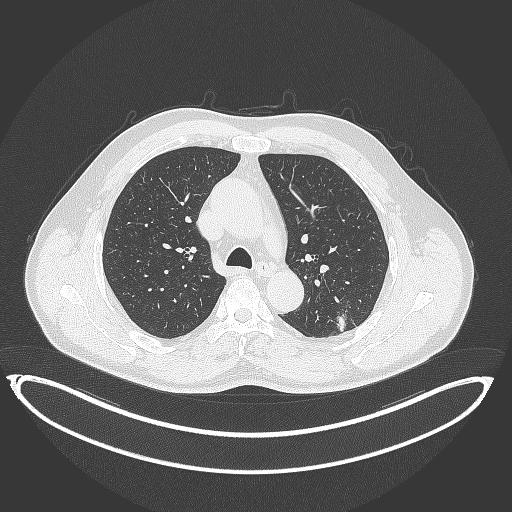
Chest CT, one axial slice; position 243 of 399 along the scan axis; lung window (W 1500 / L -600 HU); 1 mm slice thickness; 512 × 512 image matrix, field of view 469 × 469 mm. Male patient, age 58 years. From the clinical record (not read from this slice): clinical TNM (as recorded): T1c N0 M0; histopathological grade: G1-2.
Annotated regions visible in this slice (rectangle marked by the reading radiologist):
- lung tumour (recorded histology: adenocarcinoma): bounding box <331,308,353,334> (left, top, right, bottom; pixels)